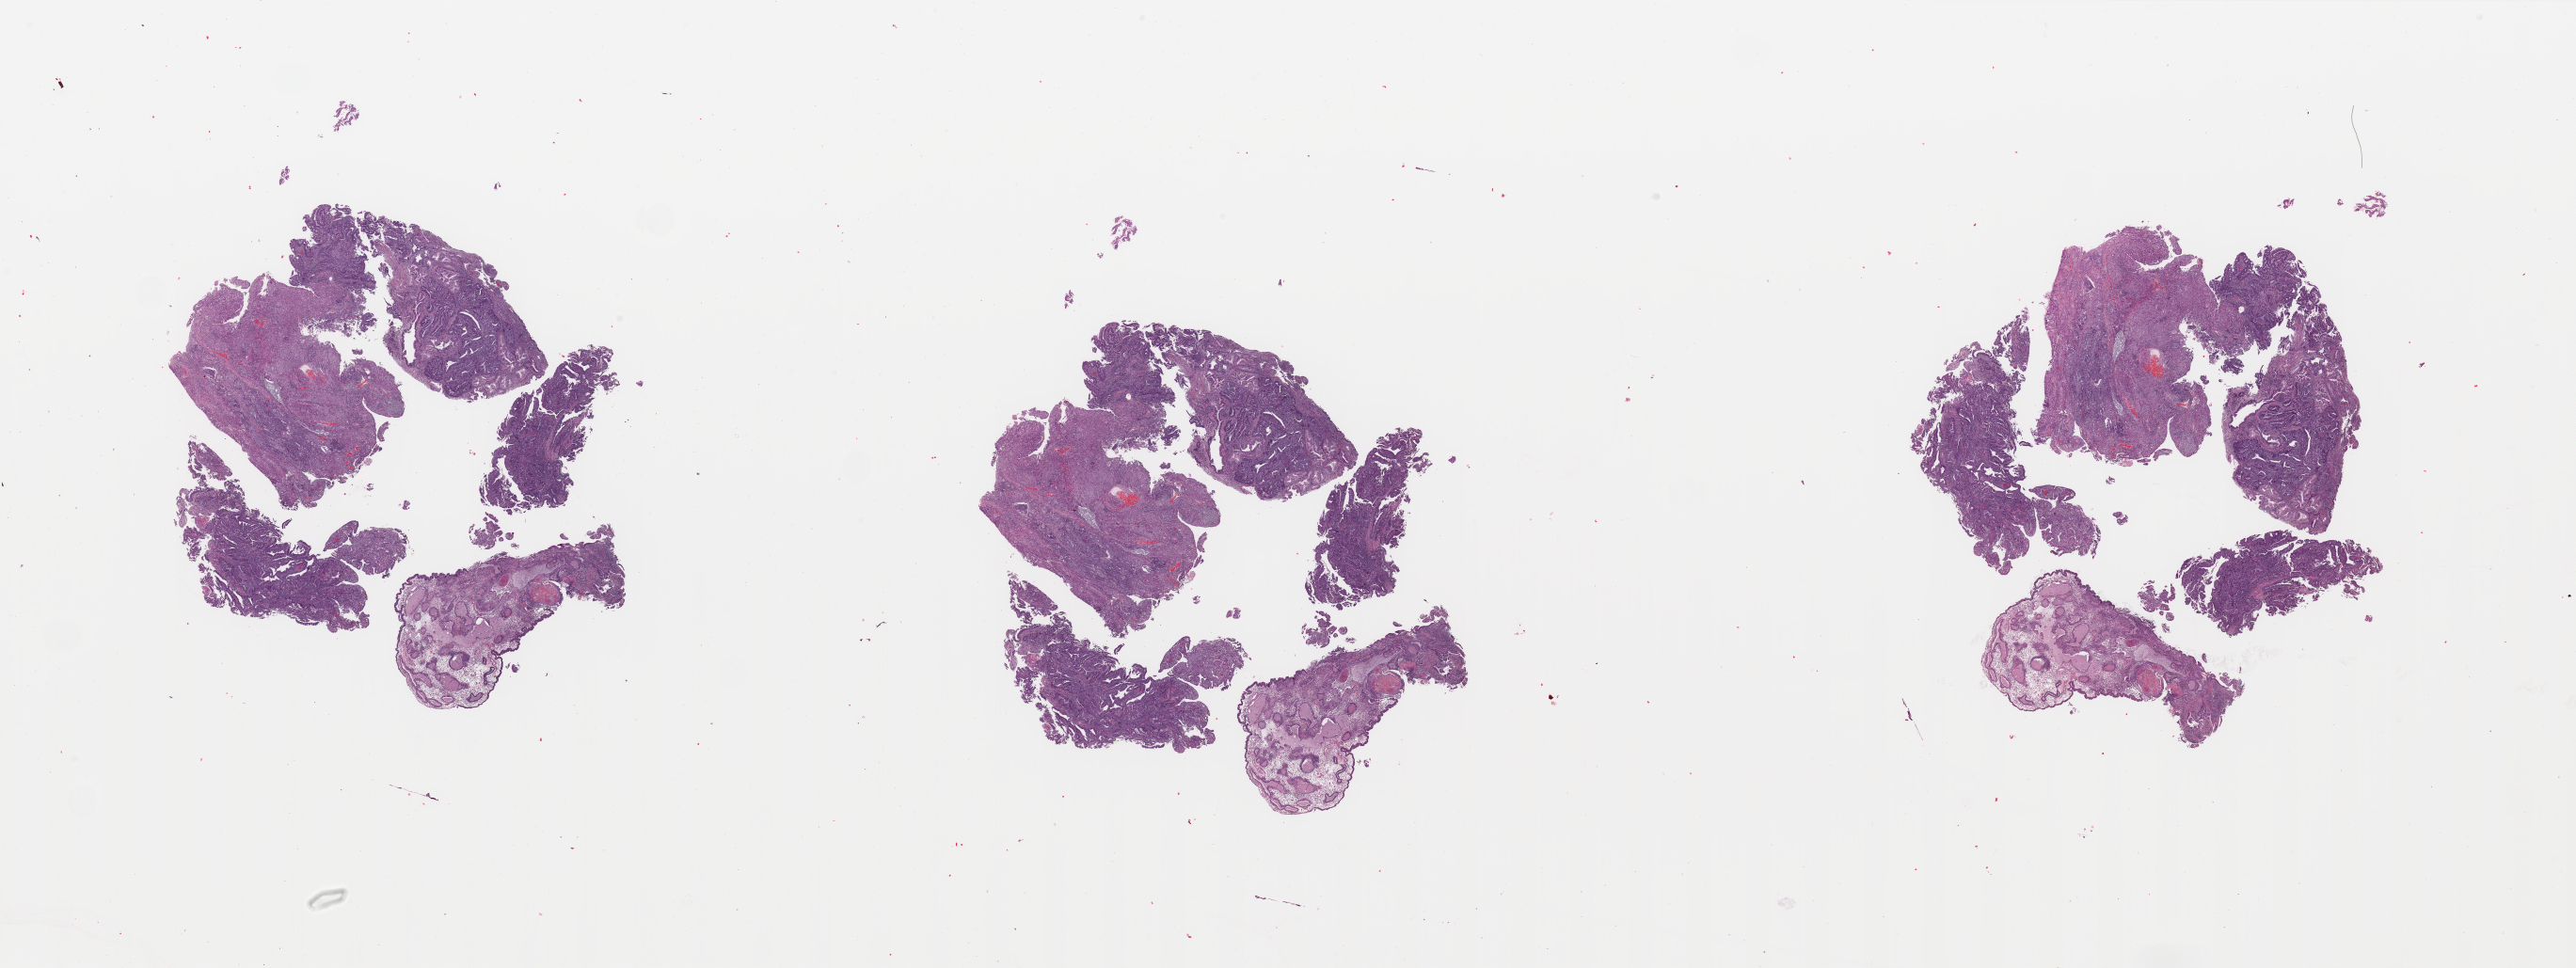
H&E-stained whole-slide image — a low-resolution overview of the entire scanned area, about 43.3 x 16.3 mm. Tumour tissue sample, uterus. 39-year-old female patient. Histologic grade: G2 (moderately differentiated).
* AJCC pathologic stage: I
* diagnosis: Endometrioid adenocarcinoma, NOS